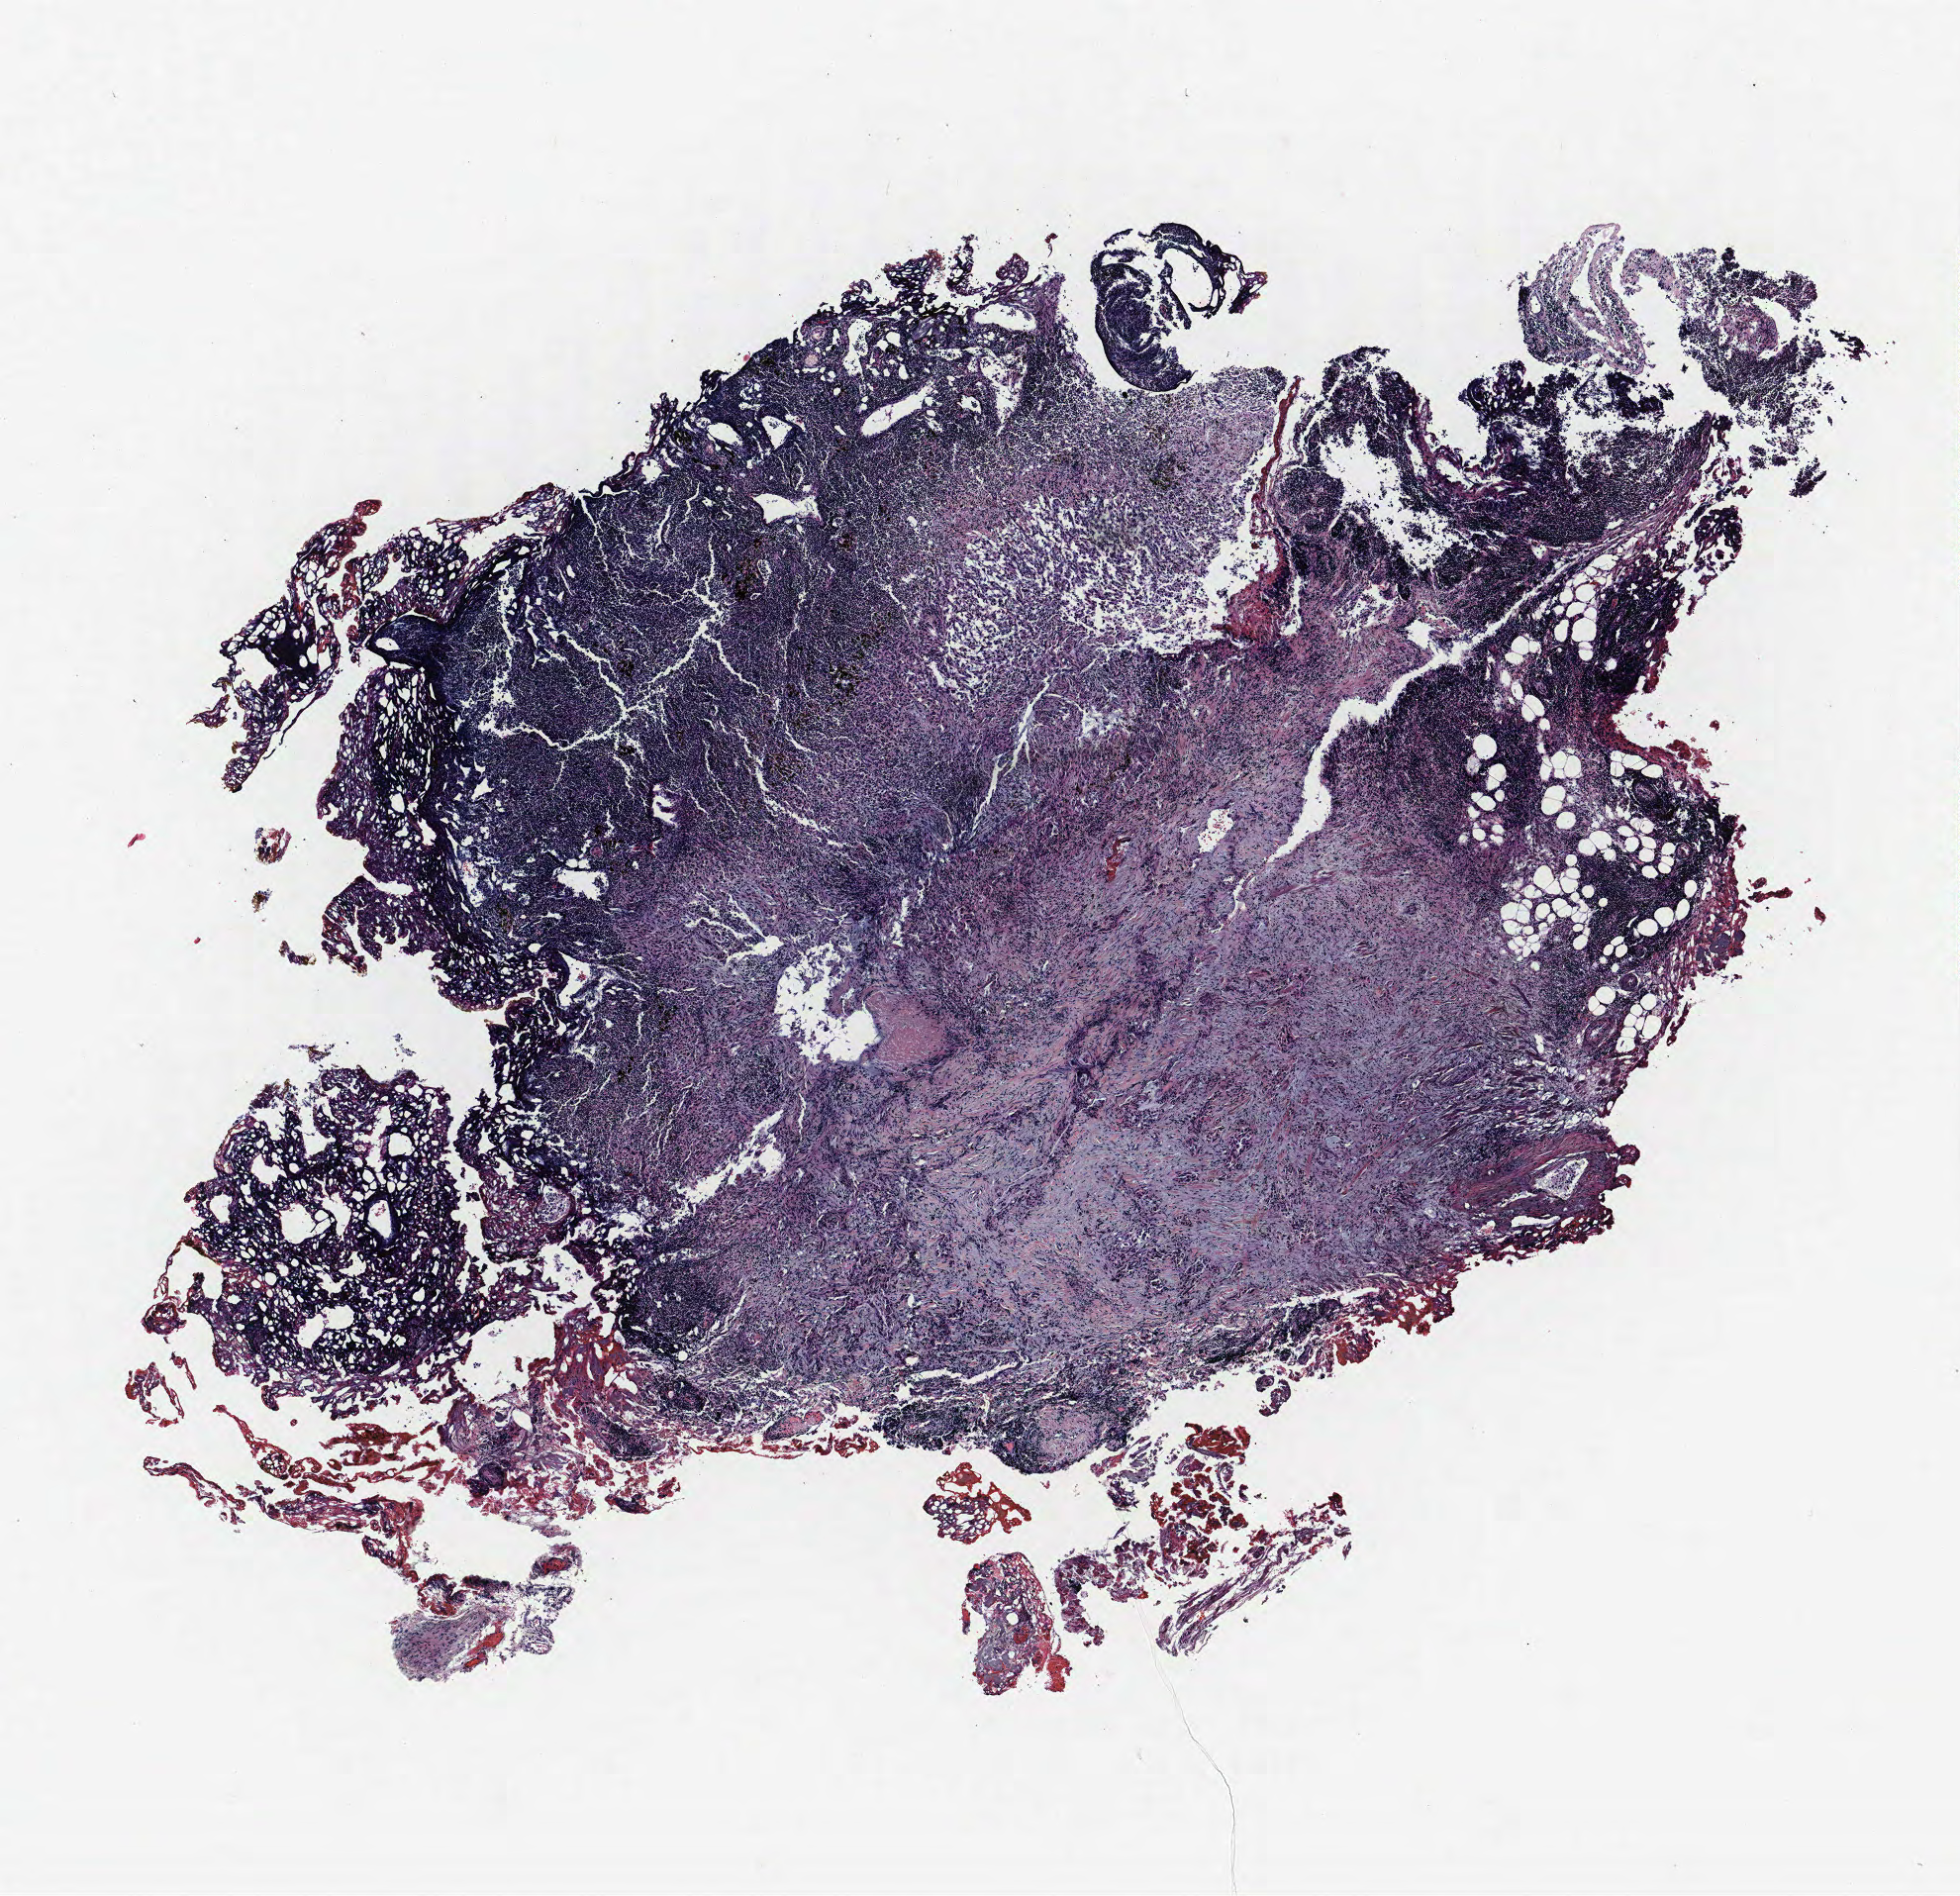
H&E-stained whole-slide image — shown as a low-resolution overview of the whole scanned area (about 7.9 x 7.7 mm). Formalin-fixed paraffin-embedded (FFPE) section. Lung tissue. Female, age 60 at enrolment. Current smoker at enrolment. Grade: moderately differentiated (G2).
* participant's lung-cancer diagnosis: Adenocarcinoma, NOS
* stage (AJCC 6th edition): IIIB
* tumour size (pathology): 28 mm
* primary tumour location (clinical record): right lower lobe
* ICD-O-3 topography: lower lobe of lung (C34.3)